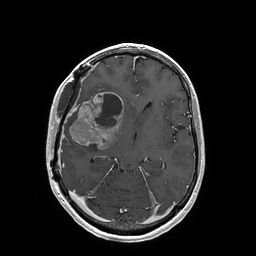
Brain MRI from a brain-tumour surgery series, one axial slice. Slice 96 of 202 in the series (ordered by position). T1-weighted post-contrast. 1 mm slice thickness. 256 × 256 image matrix, field of view 250 × 250 mm. Case-level facts recorded for this patient, not image findings: histopathology: Glioblastoma; WHO grade: 4; IDH mutation: no.
Structures marked on this image (outlined manually by an expert reader):
- tumour: bounding box (x1, y1, x2, y2) in pixels: (69, 92, 122, 150)